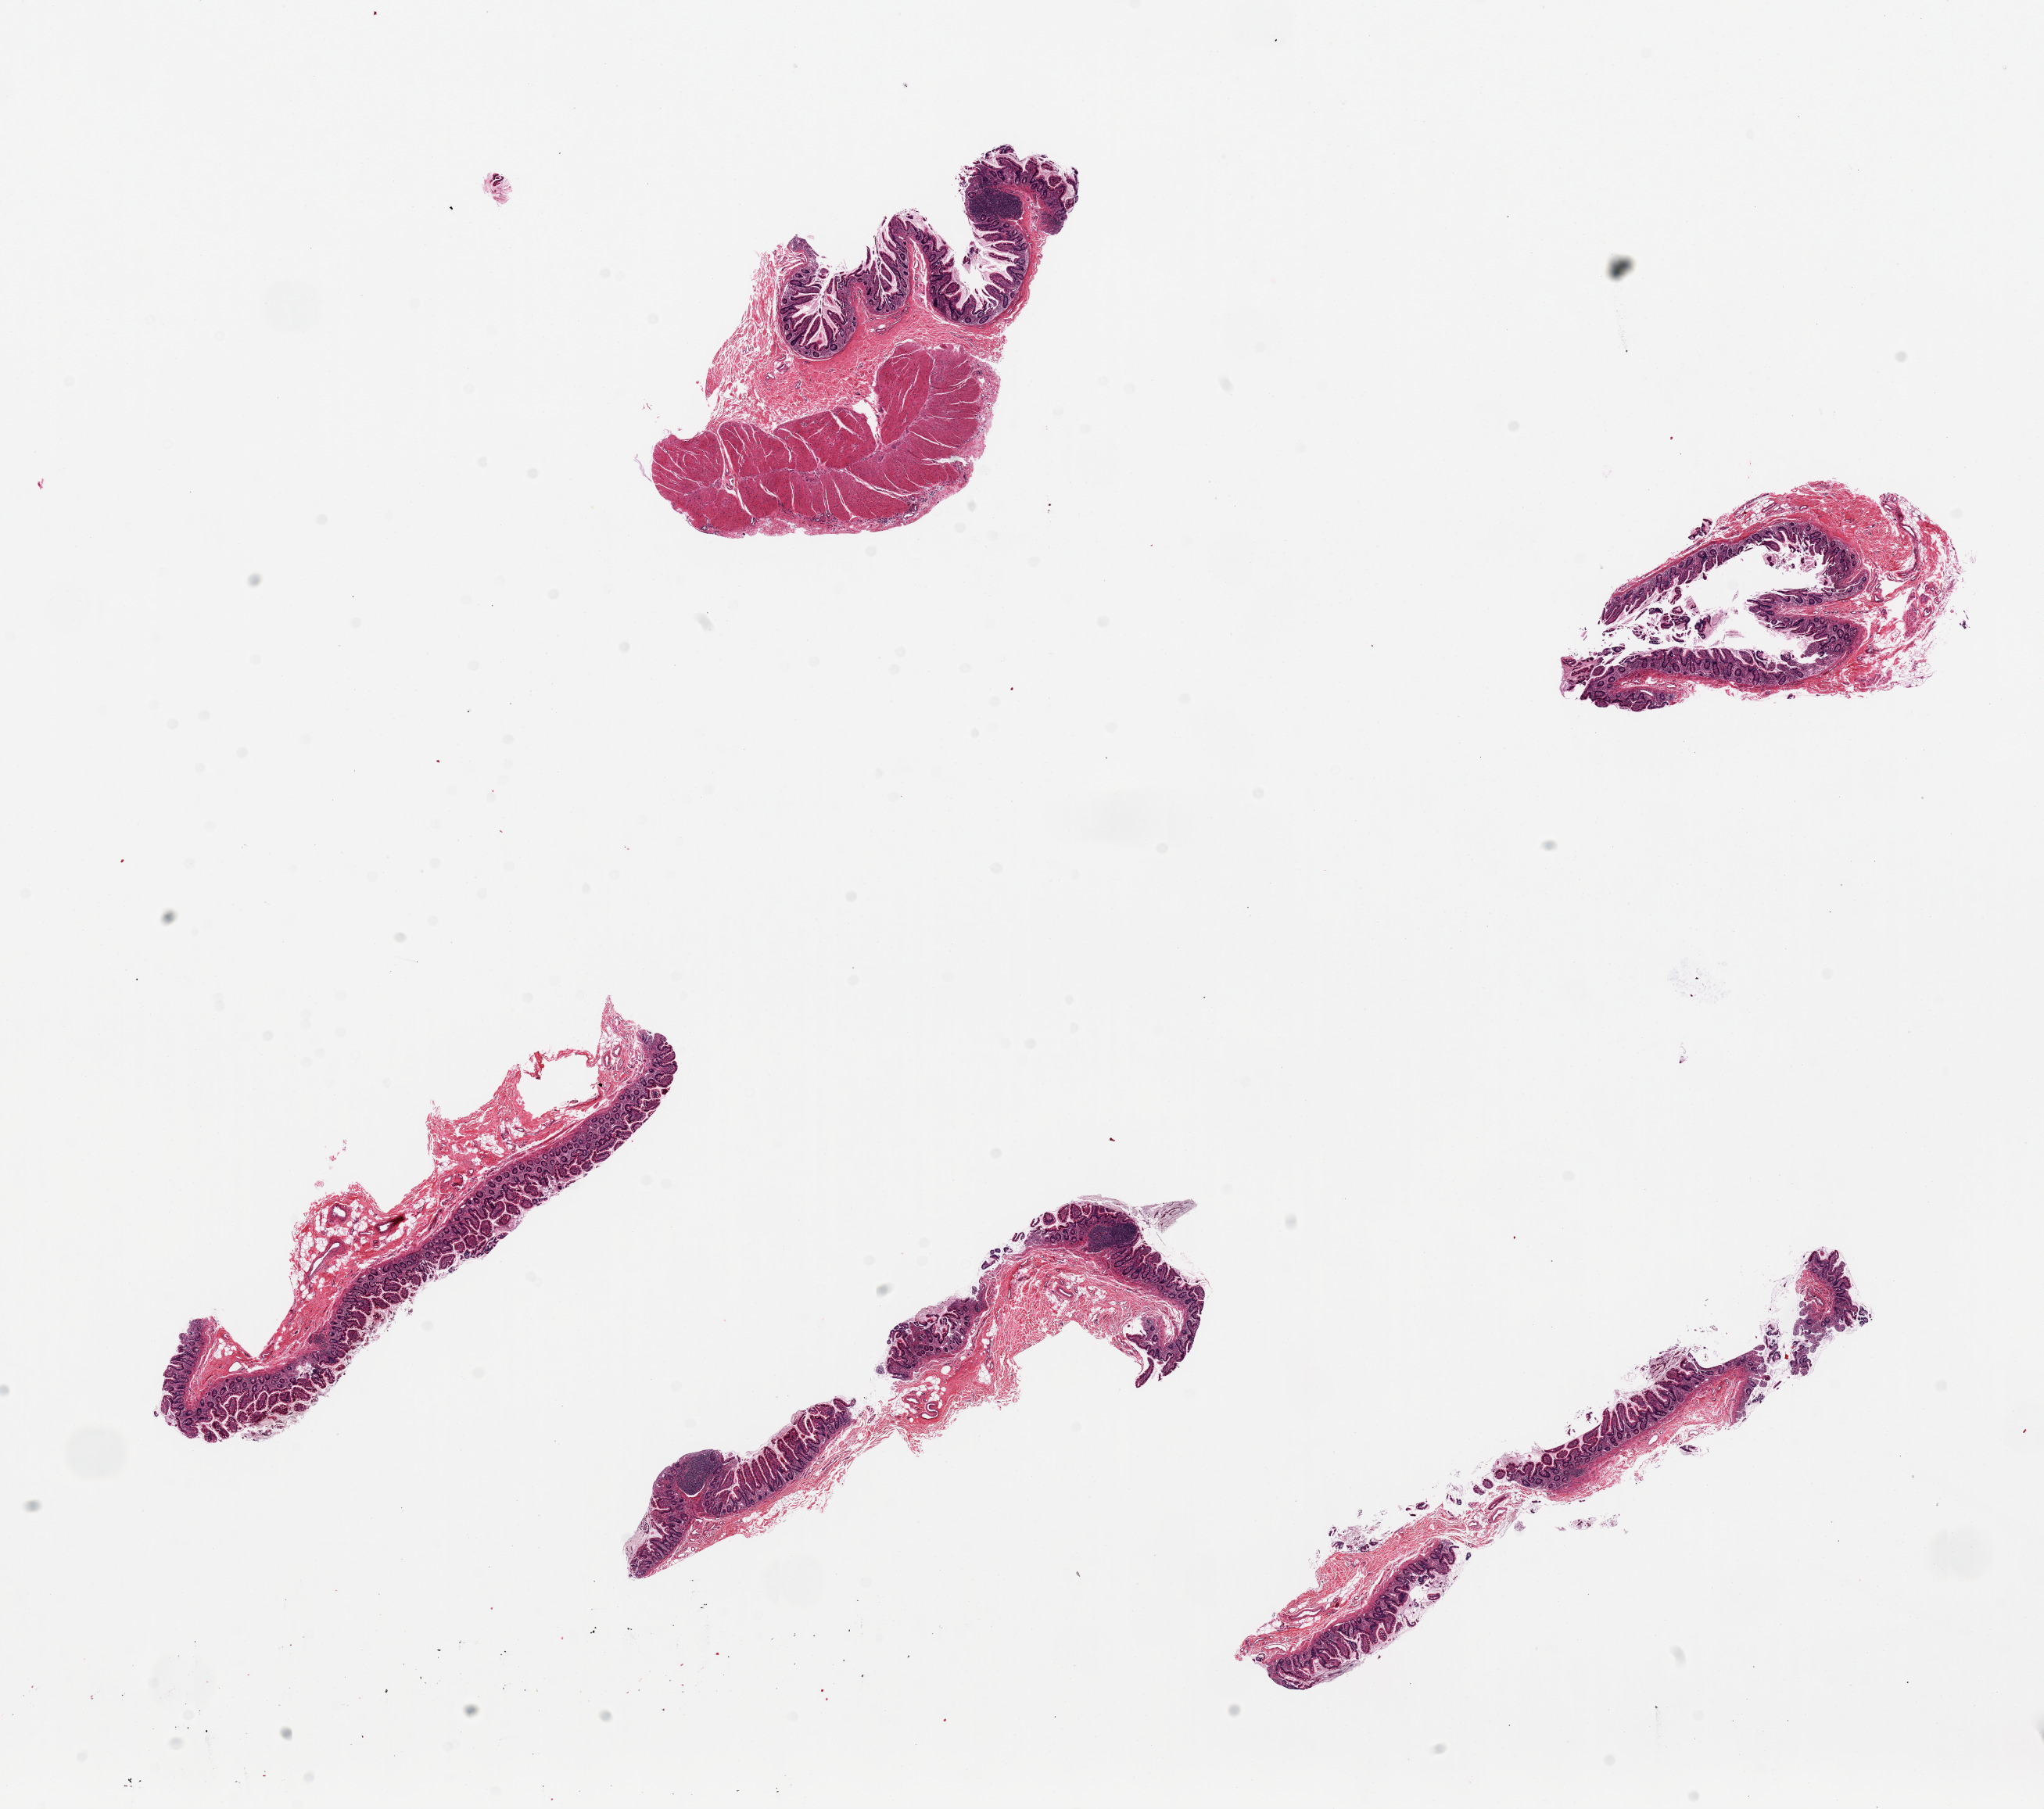
Haematoxylin and eosin whole-slide image — whole scanned area (about 20.7 x 18.3 mm) shown as a low-resolution overview; PAXgene-fixed paraffin-embedded (PFPE) section; sampled site (target tissue): ileum; tissue donor sample. Donor: female.
- review note (as recorded): 5 pieces, predominantly mucosa of small intestine with few lymphoid aggregates, small portion of muscularis